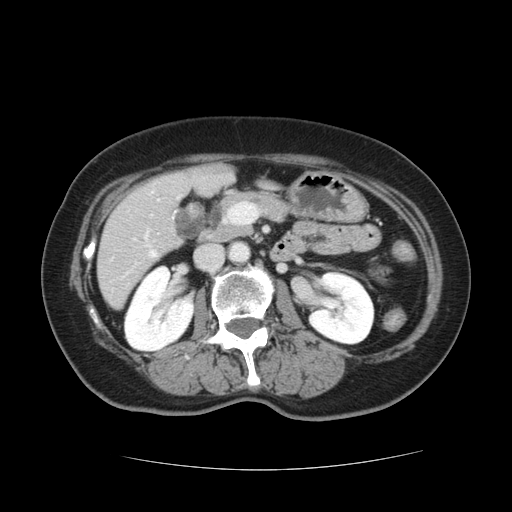
Contrast-enhanced abdominal CT, one axial slice. 120 kVp. Intravenous contrast given. Soft-tissue window (W 400 / L 40 HU). 2.5 mm slice thickness. 512 × 512 image matrix, field of view 366 × 366 mm. Female patient, age 67 years. From the clinical record (not read from this slice): diagnosis: colorectal cancer liver metastases, imaged before liver resection; multiple liver metastases: yes; largest metastasis: 3 cm; disease in both lobes: yes.
Outlined on this slice (expert manual segmentation):
- hepatic veins: bounding box [x1, y1, x2, y2] px = [151, 251, 156, 256]
- liver: [99, 165, 234, 307]
- planned liver remnant (the part of the liver to remain after resection): [99, 221, 178, 307]